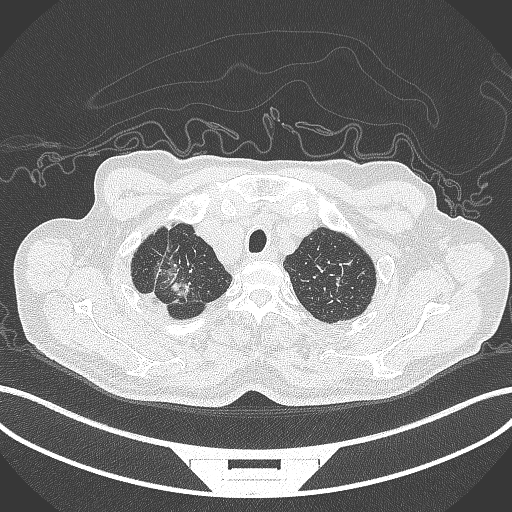
Chest CT, one axial slice; 120 kVp; lung window (W 1500 / L -600 HU); 512 × 512 image matrix. Patient: male, 69 years. Case-level facts recorded for this patient, not image findings: clinical TNM (as recorded): T1c N1 M1.
Annotated regions visible in this slice (rectangle marked by the reading radiologist):
- lung tumour (recorded histology: adenocarcinoma): box from (x=150, y=254) to (x=208, y=308) px